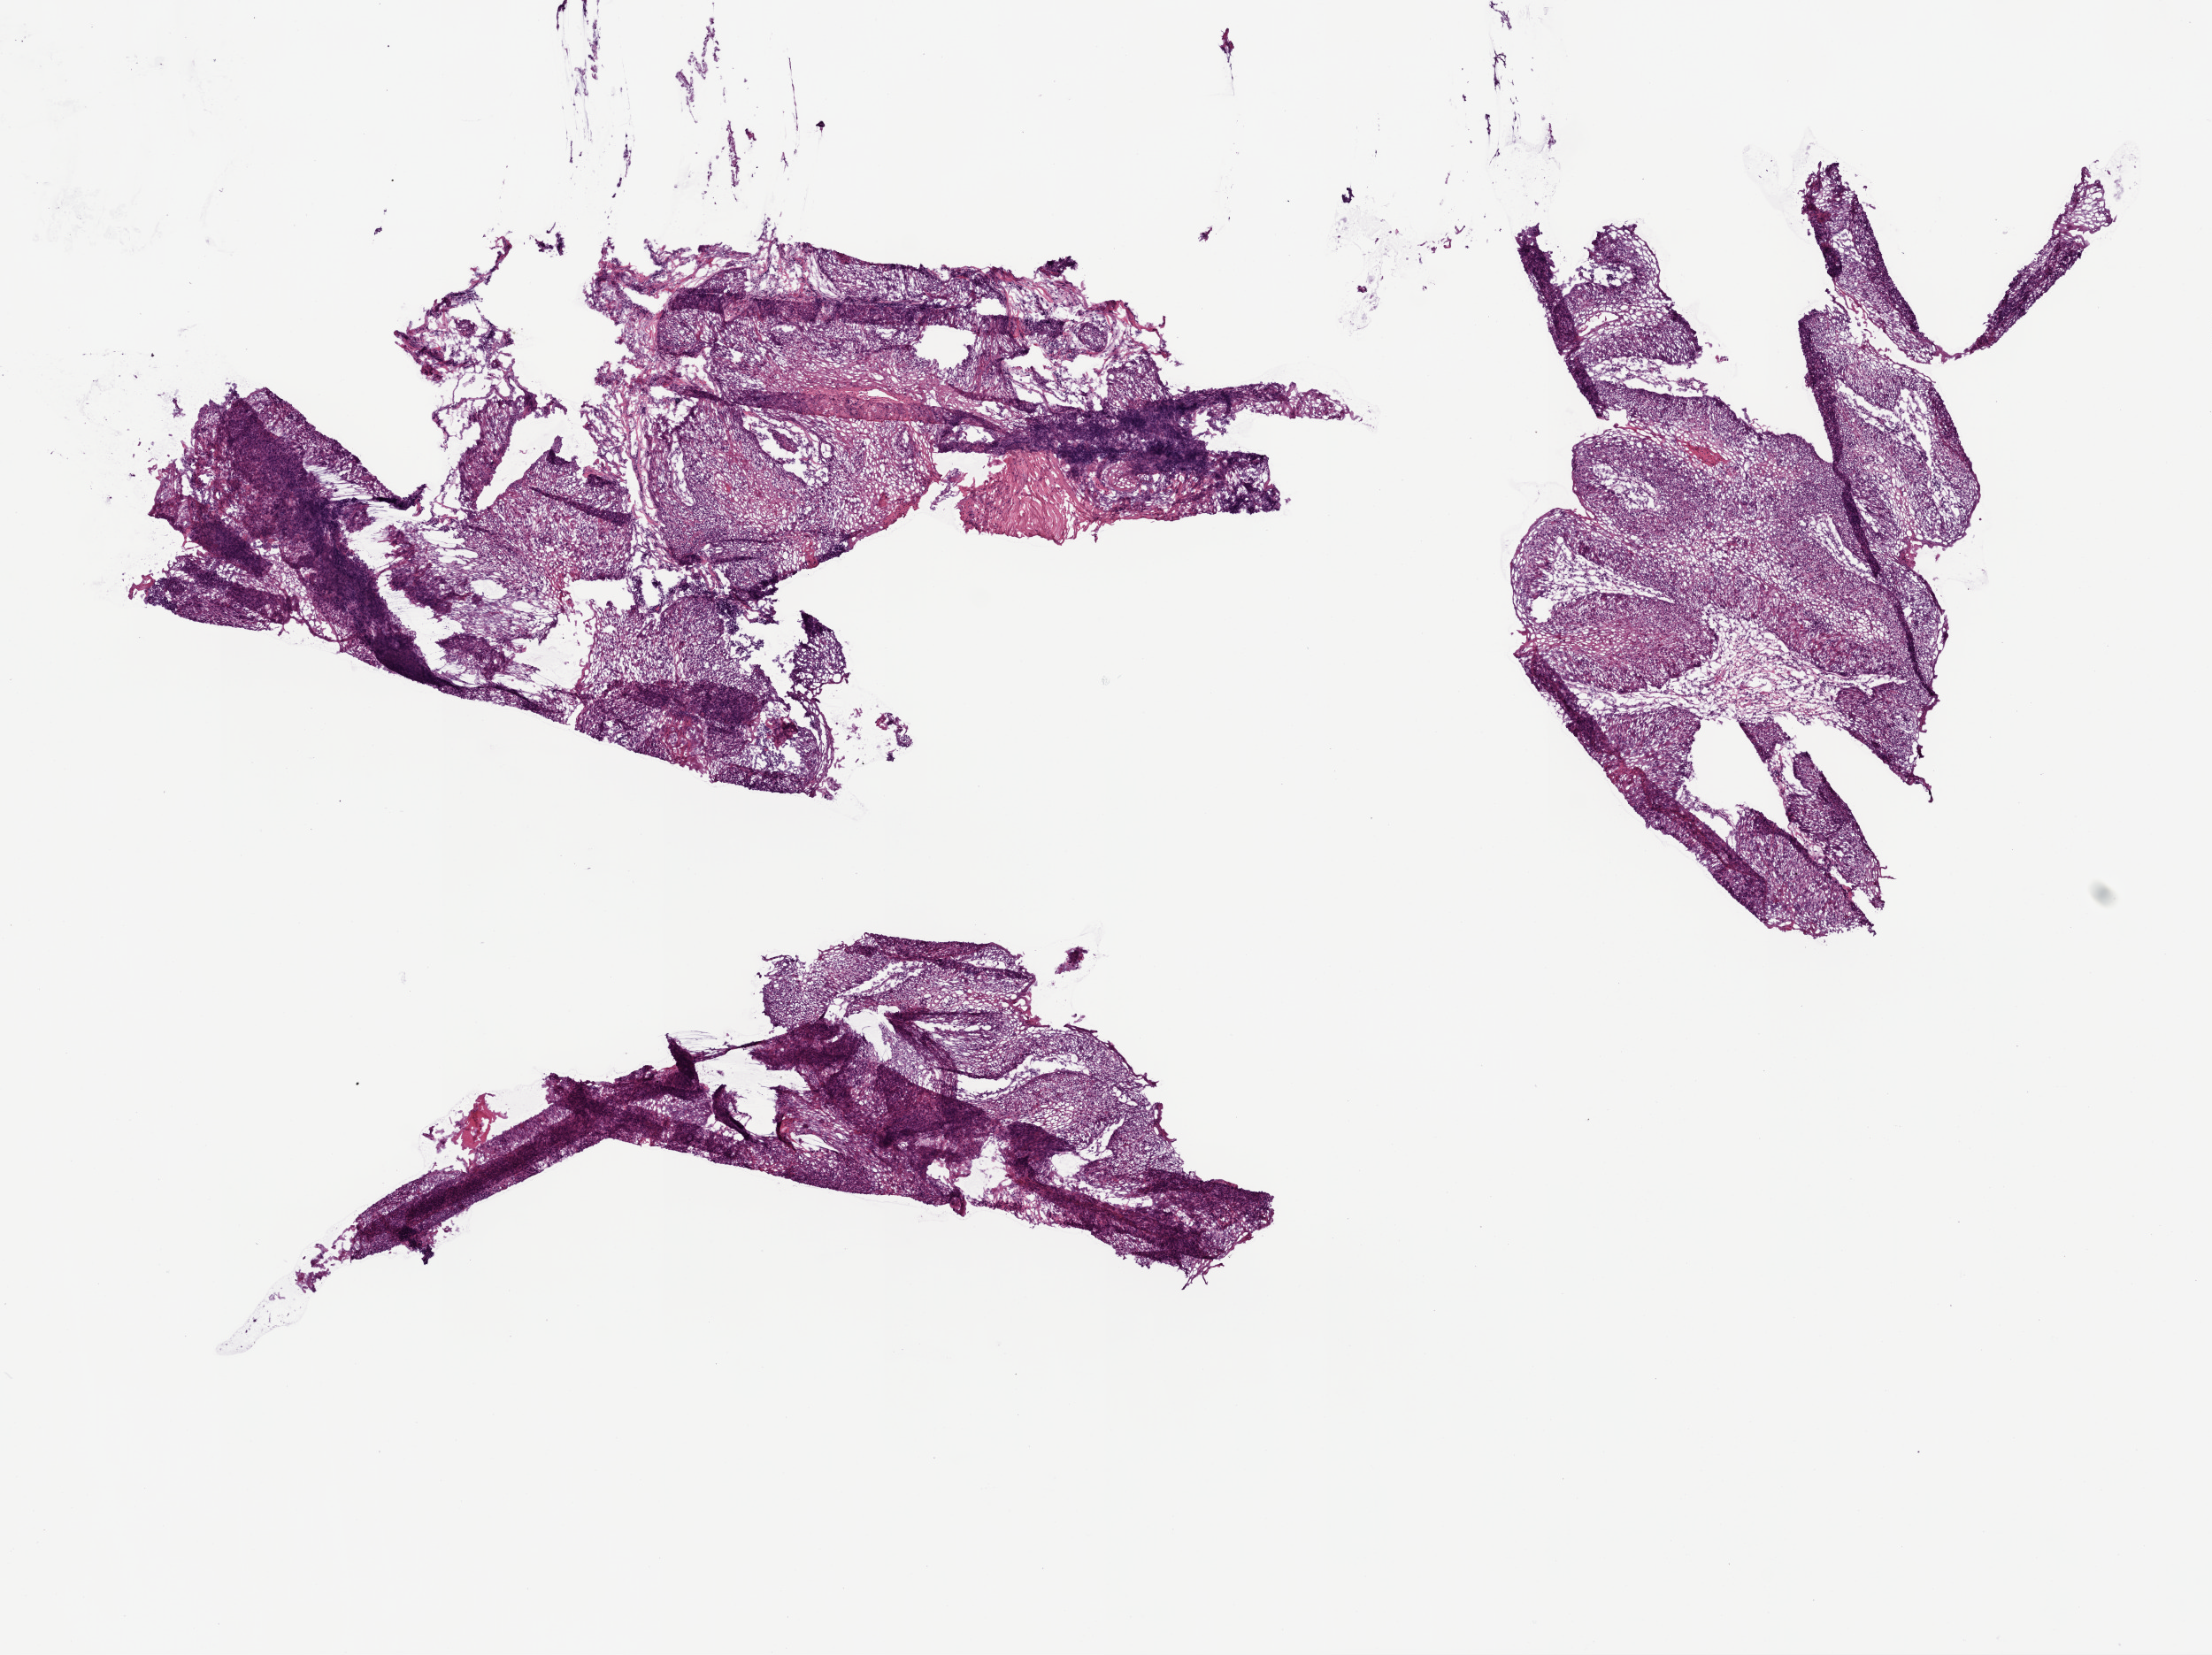
Digitized H&E tissue section (whole slide) — whole scanned area (about 10.0 x 7.5 mm) shown as a low-resolution overview; frozen section from the top of the tissue portion; primary tumour sample from the head and neck. Female patient; age at initial diagnosis 76 years. Histologic grade: G3 (poorly differentiated). Pathologist review of this section (percent, as recorded): tumour cells 80%, tumour nuclei 90%, normal cells 0%, stromal cells 20%, necrosis 0%.
Histologic diagnosis: Squamous cell carcinoma, NOS (hard palate). TNM: T4a N2b. AJCC pathologic stage: IVA (7th edition).